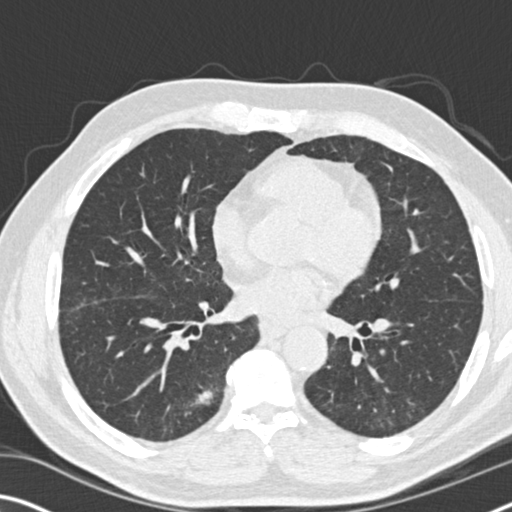
Low-dose screening chest CT, one axial slice. Lung window (W 1500 / L -600 HU). 2 mm slice thickness. 512 × 512 image matrix, field of view 340 × 340 mm.
Outlined on this slice (outlined manually by an expert reader):
- lesion 1 (tumor, lower lobe of right lung): box from (x=191, y=390) to (x=213, y=406) px